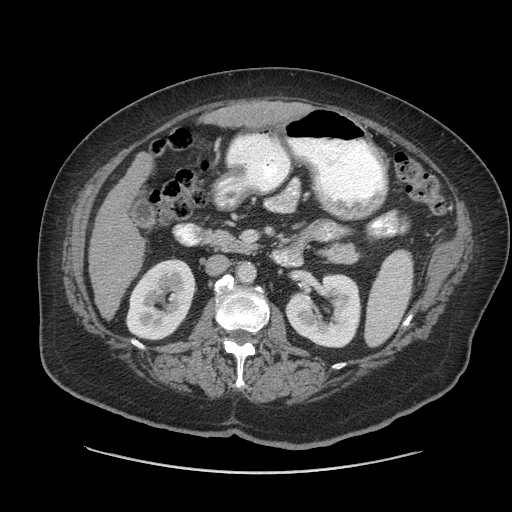
Contrast-enhanced abdominal CT (liver protocol), one axial slice. Position 22 of 91 along the scan axis. Reconstruction kernel STANDARD. 140 kVp. Soft-tissue window (W 400 / L 40 HU). 512 × 512 image matrix. Case-level facts recorded for this patient, not image findings: diagnosis: hepatocellular carcinoma (patient treated with transarterial chemoembolisation; whether this scan precedes or follows treatment is not stated here); TNM stage (as recorded): Stage-I; Child-Pugh class: A; tumour differentiation: well differentiated; tumour nodularity: uninodular.
Annotated regions visible in this slice (semi-automatically segmented with operator editing):
- liver parenchyma outside the tumour (the mass and vessels are separate outlines, so this box may not span the whole liver): bounding box [x1, y1, x2, y2] px = [88, 152, 152, 318]